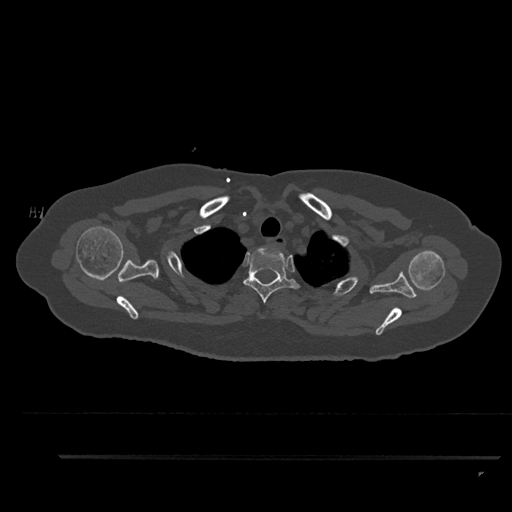
CT including the spine, one axial slice; slice 725 of 797 in the series (ordered by position); bone window (W 1800 / L 400 HU); 512 × 512 image matrix, field of view 408 × 408 mm. Patient: female, 44 years. From the clinical record (not read from this slice): primary cancer: renal; vertebrae with lytic lesions (as recorded): L1.
Structures marked on this image (semi-automatically segmented with operator editing):
- T2 vertebra: bounding box [x1, y1, x2, y2] px = [243, 248, 301, 303]